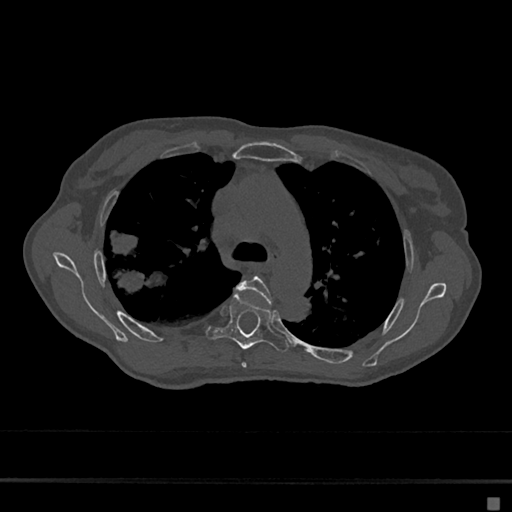
CT including the spine, one axial slice; position 471 of 797 along the scan axis; bone window (W 1800 / L 400 HU); 0.5 mm slice thickness; 512 × 512 image matrix. Female patient, age 68 years. From the clinical record (not read from this slice): primary cancer: renal.
Outlined on this slice (semi-automatically segmented with operator editing):
- T4 vertebra: bounding box [x1, y1, x2, y2] px = [236, 276, 272, 368]
- T5 vertebra: [208, 294, 288, 351]